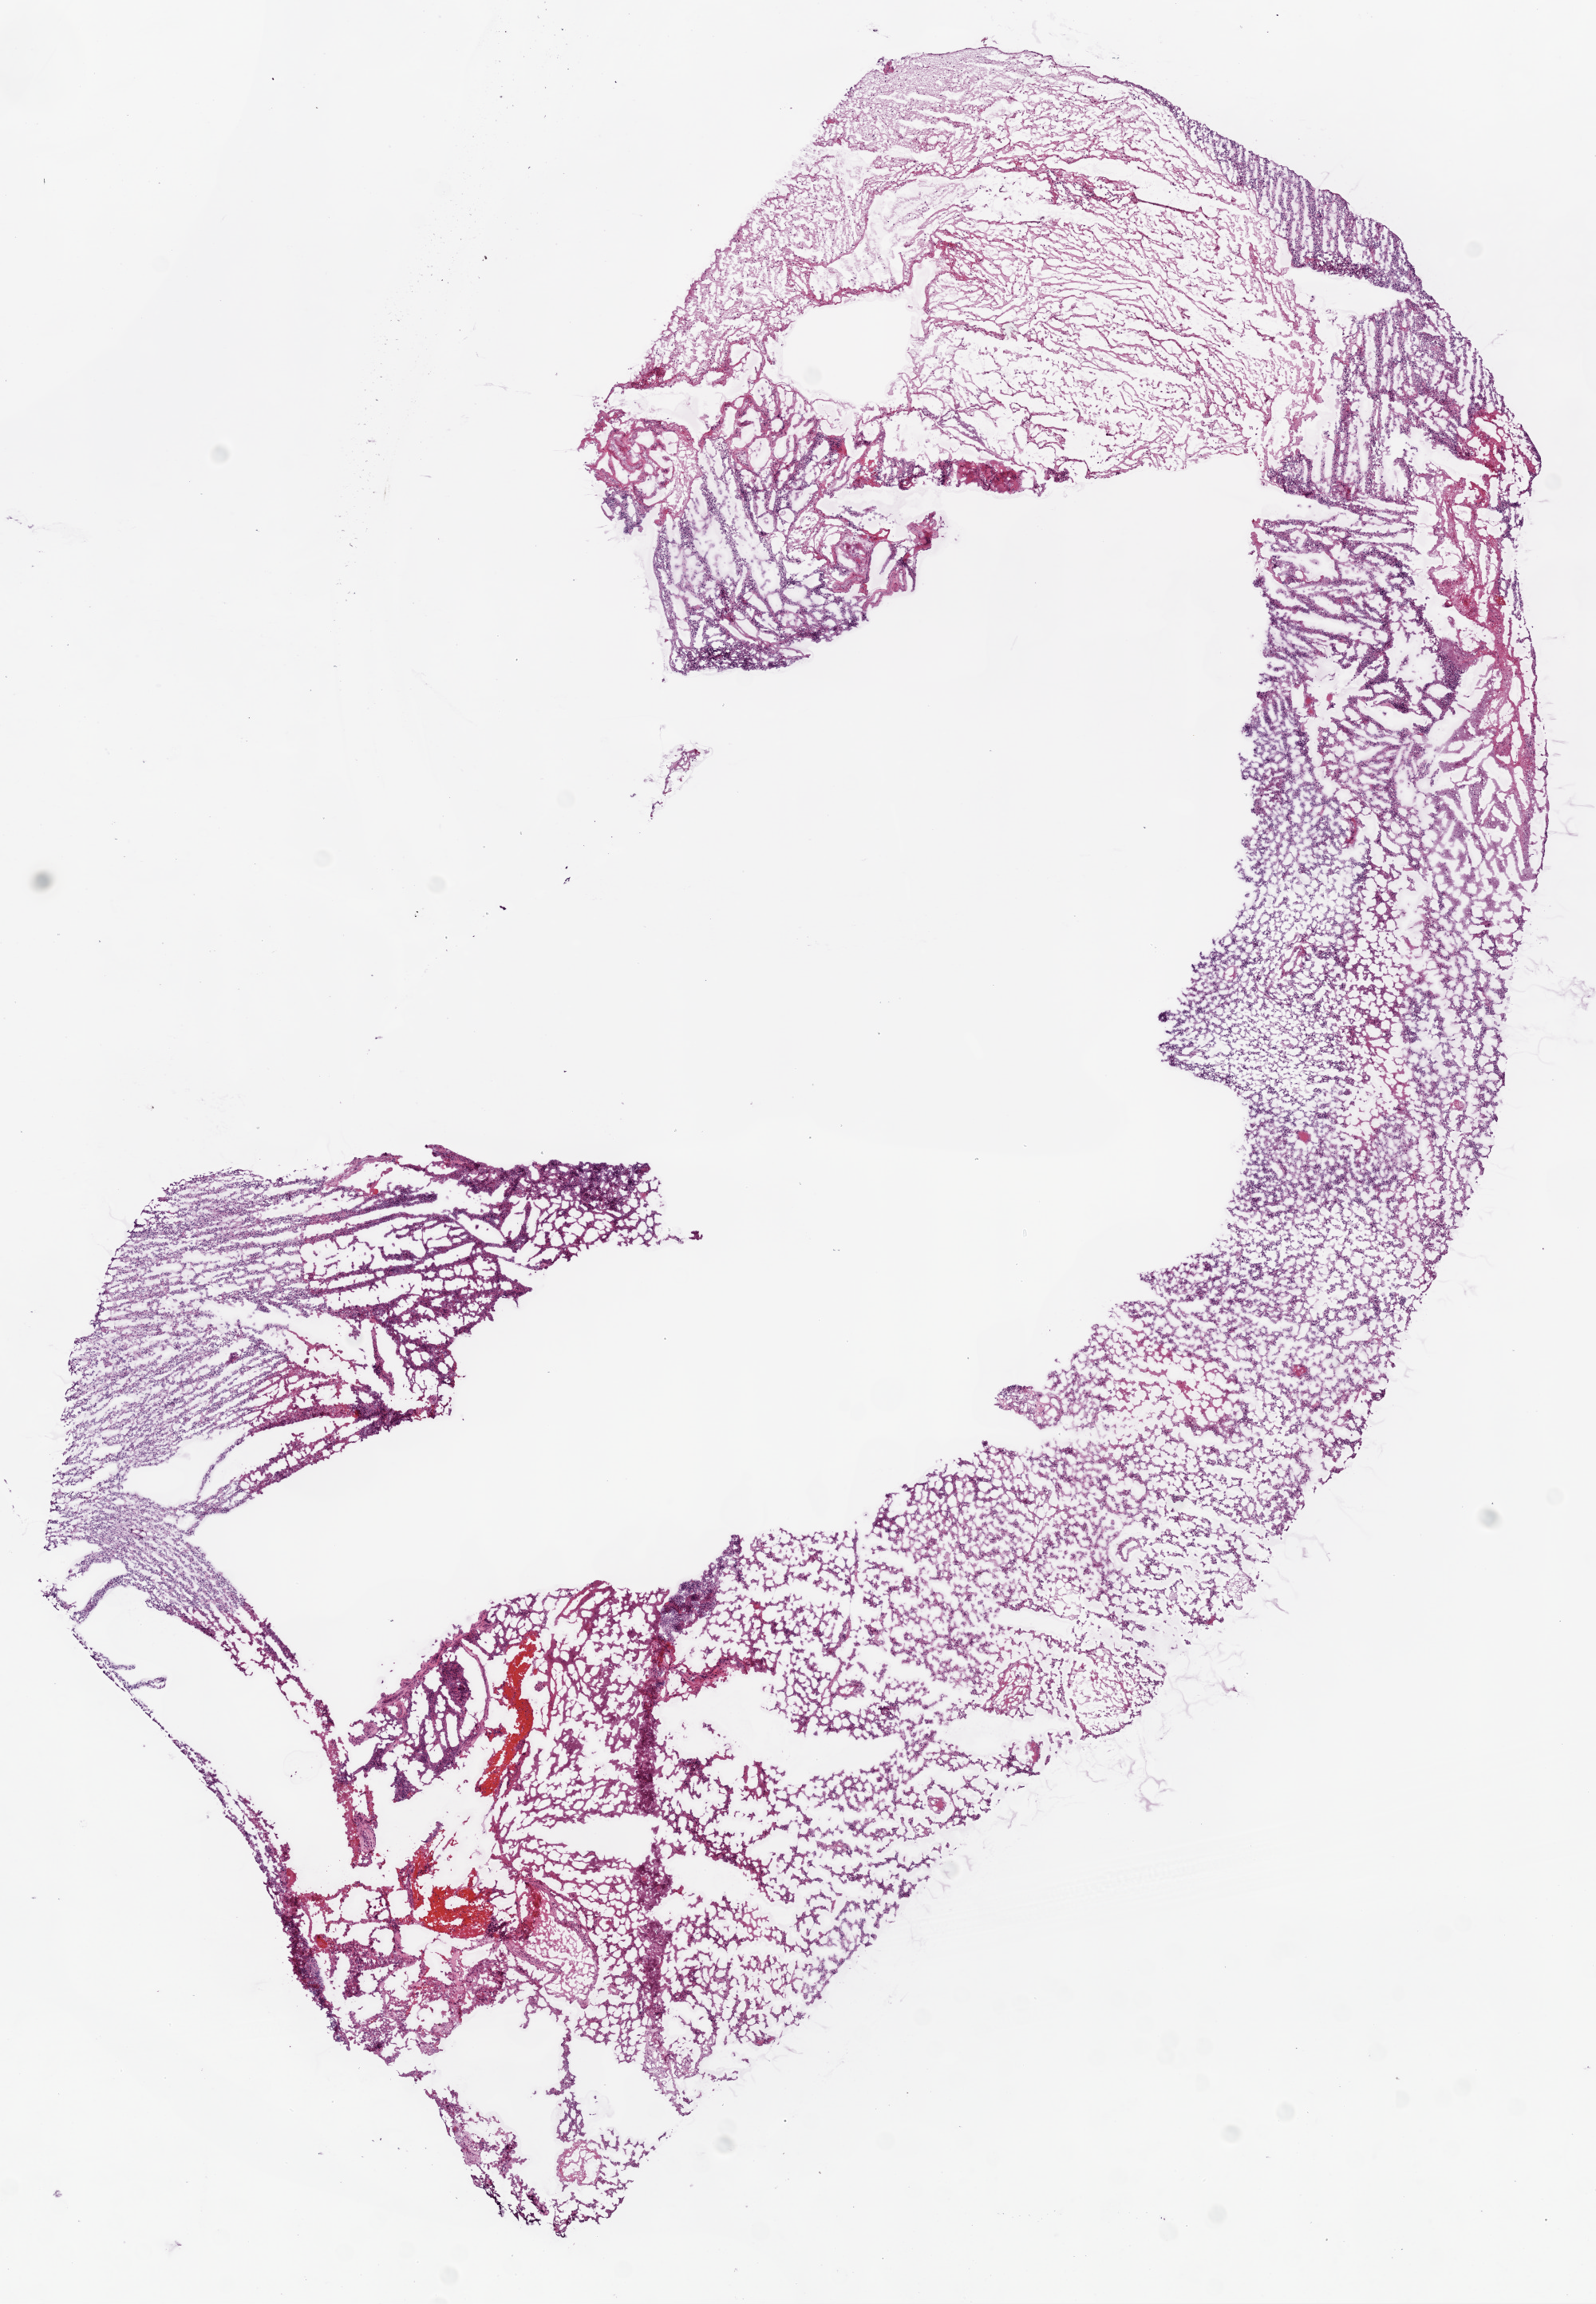
Whole-slide histology image, H&E, a low-resolution overview of the entire scanned area, about 8.0 x 11.6 mm (from a 20x scan). Frozen section from the bottom of the tissue portion. Primary tumour sample from the brain. Female patient; age at initial diagnosis 52 years. Pathologist review of this section (percent, as recorded): tumour cells 60%, tumour nuclei 85%.
Histologic diagnosis: Glioblastoma.